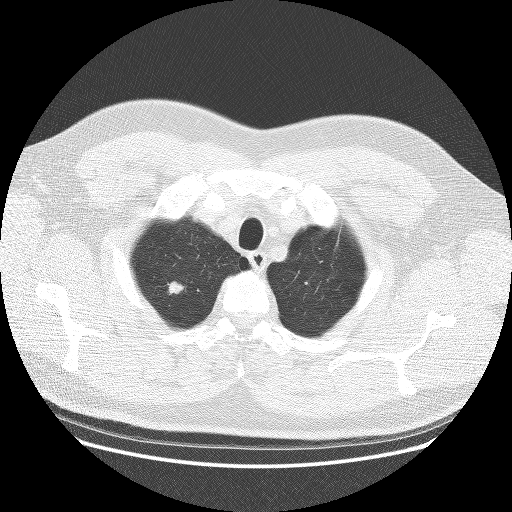
Chest CT (low-dose screening protocol), one axial image. First (baseline) screen. Lung window (W 1500 / L -600 HU). 2.5 mm slice thickness. Lung (sharp) reconstruction kernel (BONE). Slice 14 of 111 in the series. 512 × 512 image matrix, field of view 389 × 389 mm. Male participant, aged 65 years at enrolment.
Expert-annotated lung lesion, bounding box <150,269,200,310> (left, top, right, bottom; pixels). Screening reader's record for this exam (one nodule recorded; not confirmed to be the boxed lesion): non-calcified nodule or mass ≥4 mm, right upper lobe, 11 × 9 mm, poorly defined margins, soft tissue attenuation. Official screen result: positive, change unspecified: nodule(s) >= 4 mm or enlarging nodule(s), mass(es), or other non-specific abnormalities suspicious for lung cancer.